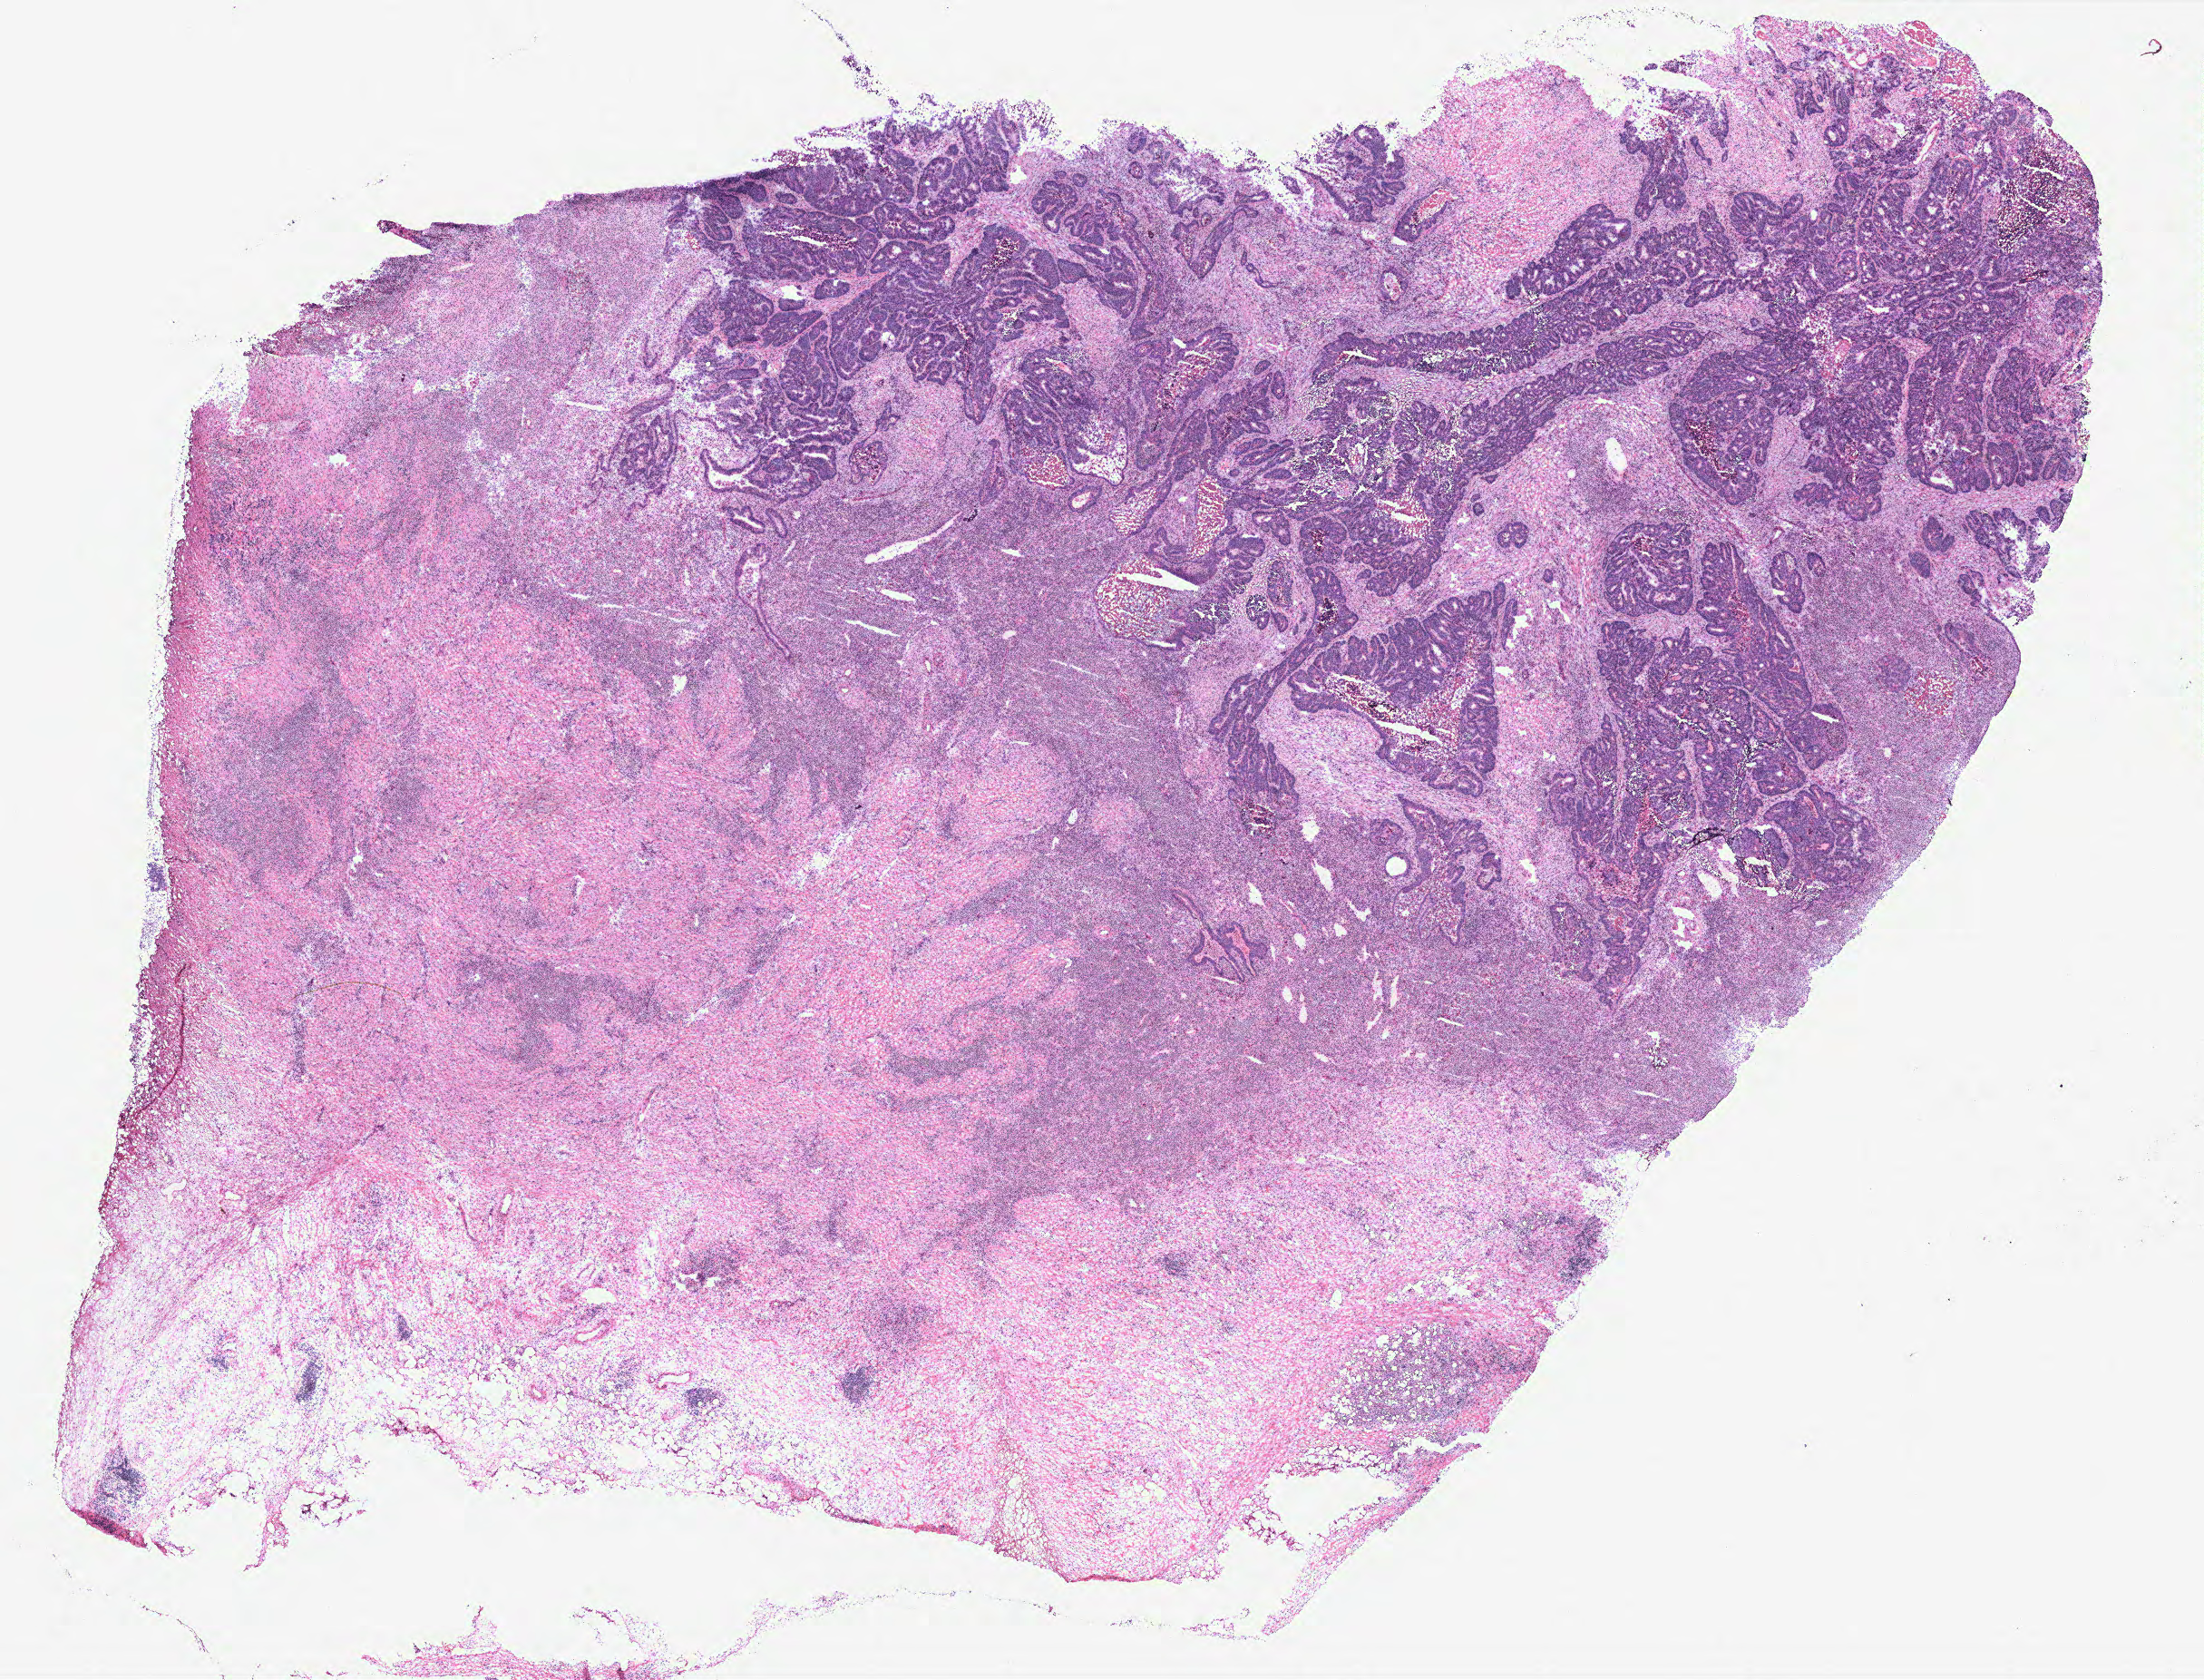
Hematoxylin and eosin (H&E) stained whole-slide image — low-resolution overview of the scanned area, about 19.4 x 14.8 mm (from a 40x scan). Tumour tissue sample, colon. Patient: male, age 65 years.
AJCC pathologic stage: IIA. Primary tumour site (as recorded): colon. Histologic diagnosis: Adenocarcinoma, NOS.